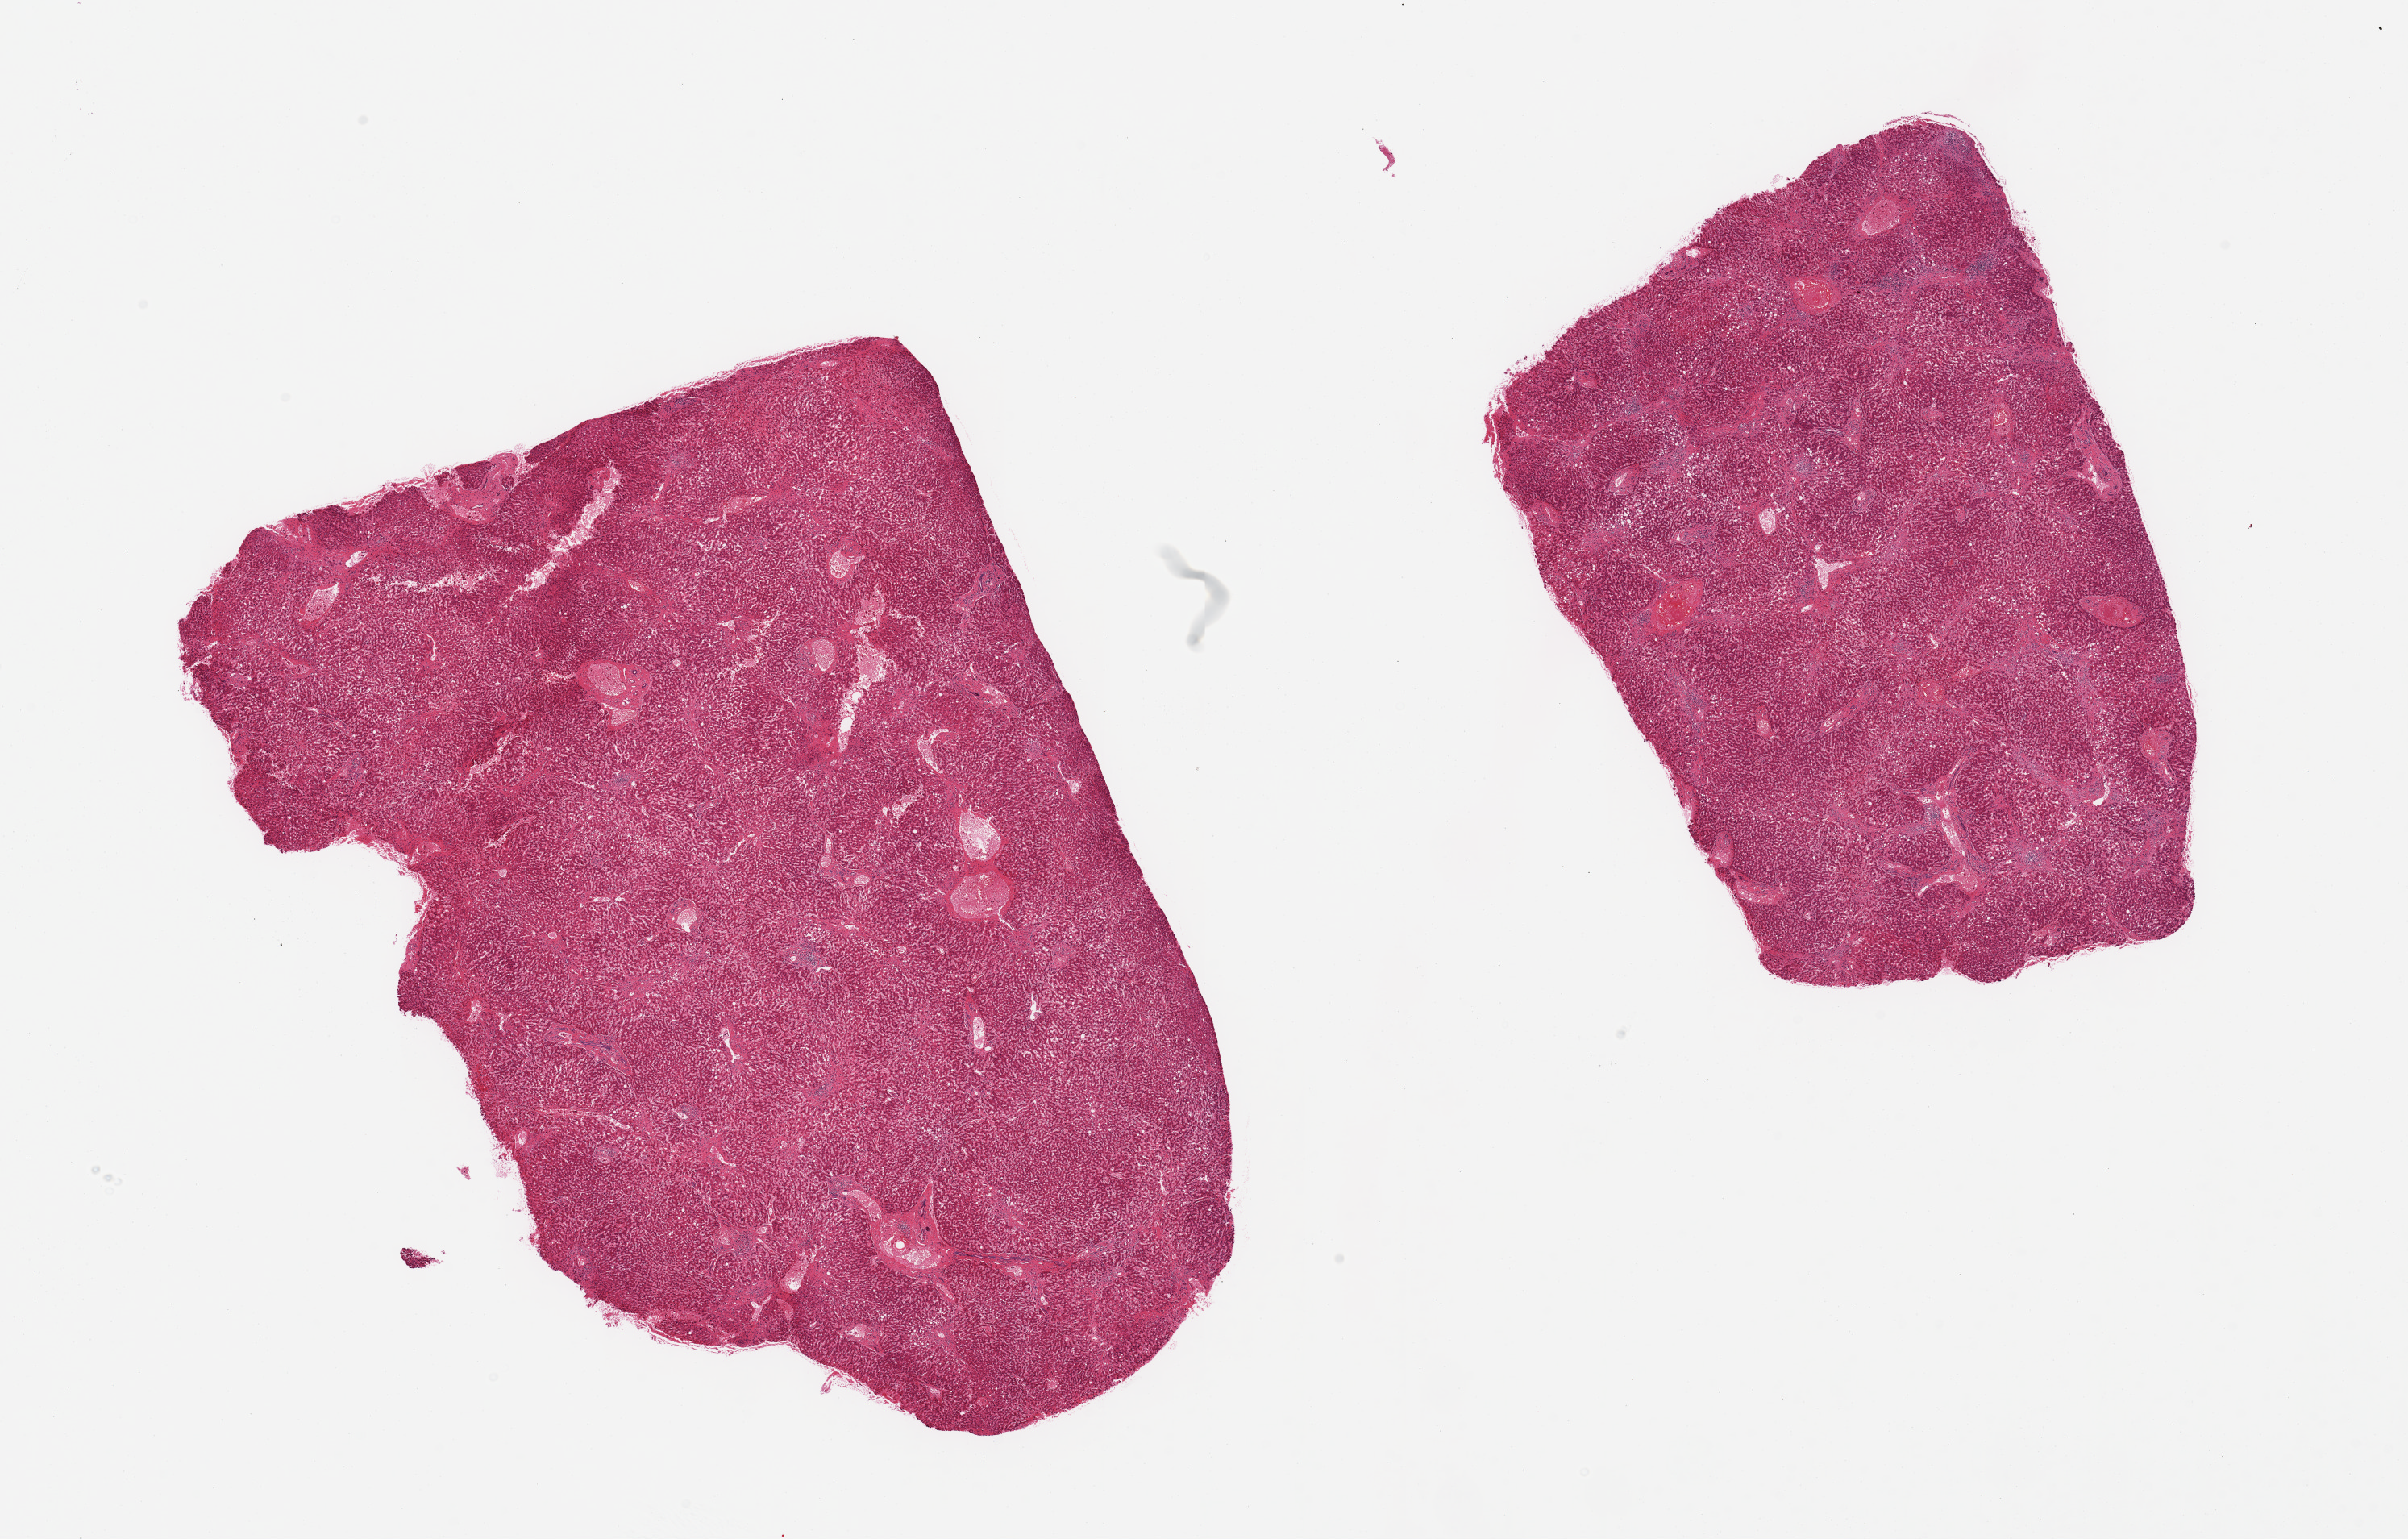
Hematoxylin and eosin (H&E) whole-slide image, a low-resolution overview of the entire scanned area, about 23.6 x 15.1 mm (acquisition: 20x scan), PAXgene-fixed paraffin-embedded (PFPE) section, sampled site (target tissue): liver, donor tissue sample. Donor: male.
Pathologist's review note for this sample: 2 pieces, moderate macrovesicular steatosis and bridging fibrosis approaching early cirrhosis.